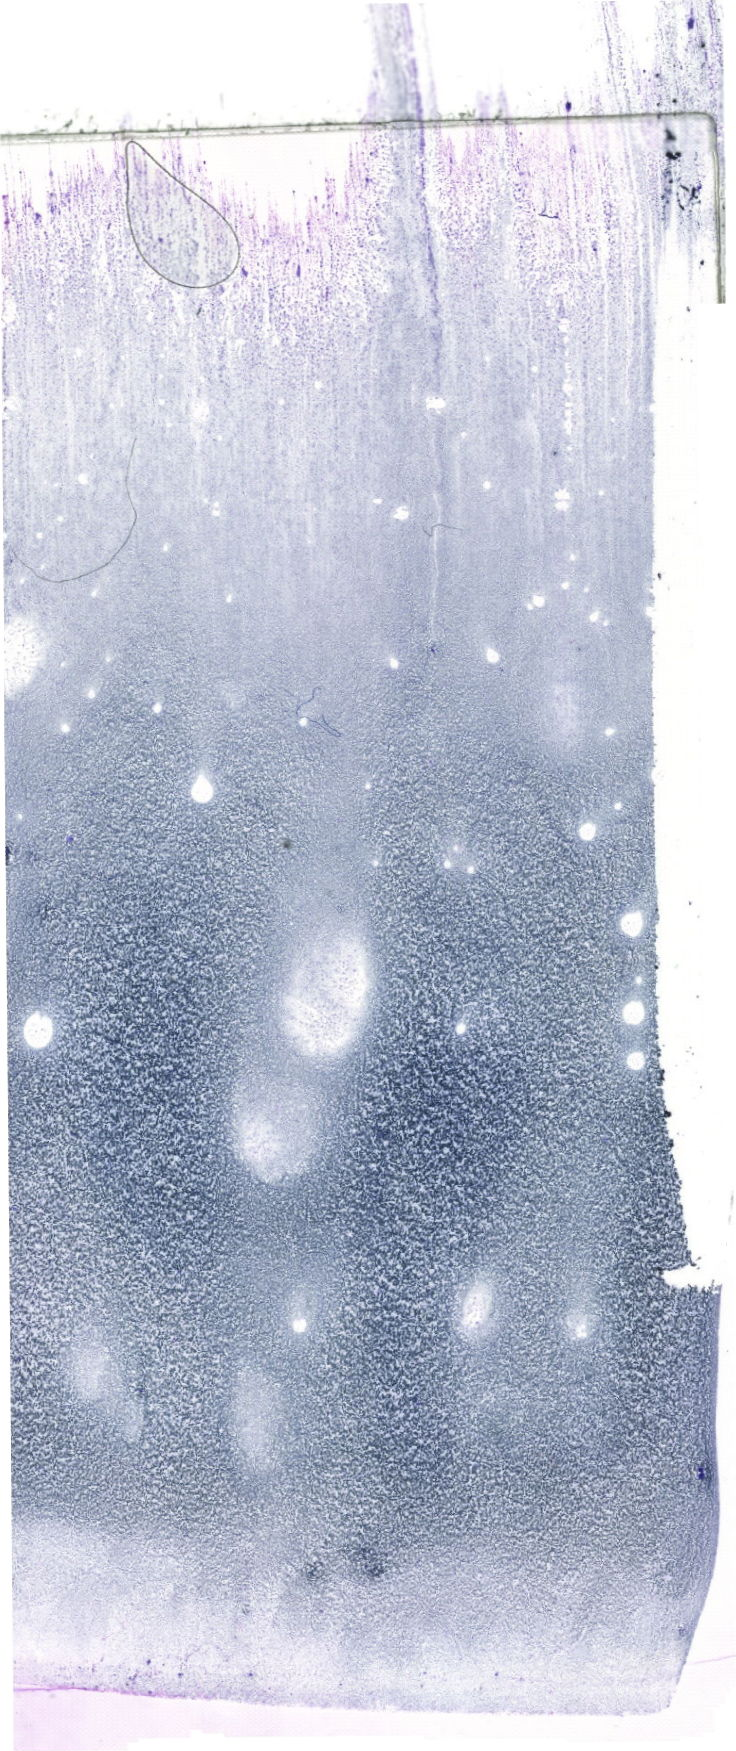
Bone marrow aspirate smear, May-Grünwald-Giemsa (MGG) stain, whole-slide image — whole scanned area (about 20.9 x 49.6 mm) shown as a low-resolution overview. Male patient.
- diagnosis: B Acute Lymphoblastic Leukemia